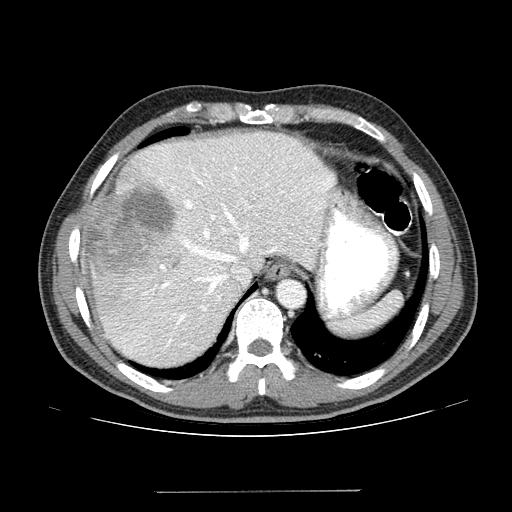
Contrast-enhanced abdominal CT (liver protocol), one axial slice. Position 107 of 131 along the scan axis. One of 2 acquisitions stored at this slice position. Soft-tissue window (W 400 / L 40 HU). 2.5 mm slice thickness. 512 × 512 image matrix, field of view 380 × 380 mm. From the clinical record (not read from this slice): diagnosis: hepatocellular carcinoma (patient treated with transarterial chemoembolisation; whether this scan precedes or follows treatment is not stated here); TNM stage (as recorded): Stage-I; Child-Pugh class: A; tumour nodularity: uninodular.
Outlined on this slice (semi-automatically segmented with operator editing):
- abdominal aorta: bounding box <279,281,304,307> (left, top, right, bottom; pixels)
- liver parenchyma outside the tumour (the mass and vessels are separate outlines, so this box may not span the whole liver): <80,132,336,366>
- mass: <81,176,176,282>
- liver vessels: <115,137,333,353>